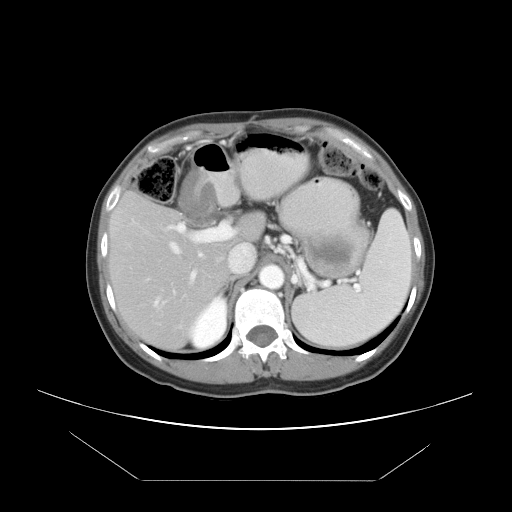
Contrast-enhanced abdominal CT, one axial slice; slice 30 of 45 in the series (ordered by position); 120 kVp; intravenous contrast given; soft-tissue window (W 400 / L 40 HU); 5 mm slice thickness; 512 × 512 image matrix, field of view 405 × 405 mm. Female patient, age 52 years. Case-level facts recorded for this patient, not image findings: diagnosis: colorectal cancer liver metastases, imaged before liver resection; multiple liver metastases: yes; largest metastasis: 2.5 cm; chemotherapy before resection: yes.
Annotated regions visible in this slice (expert manual segmentation):
- hepatic veins: bounding box <128,215,182,305> (left, top, right, bottom; pixels)
- liver: <111,195,261,348>
- planned liver remnant (the part of the liver to remain after resection): <111,195,261,340>
- portal vein (with intrahepatic branches): <167,222,233,283>